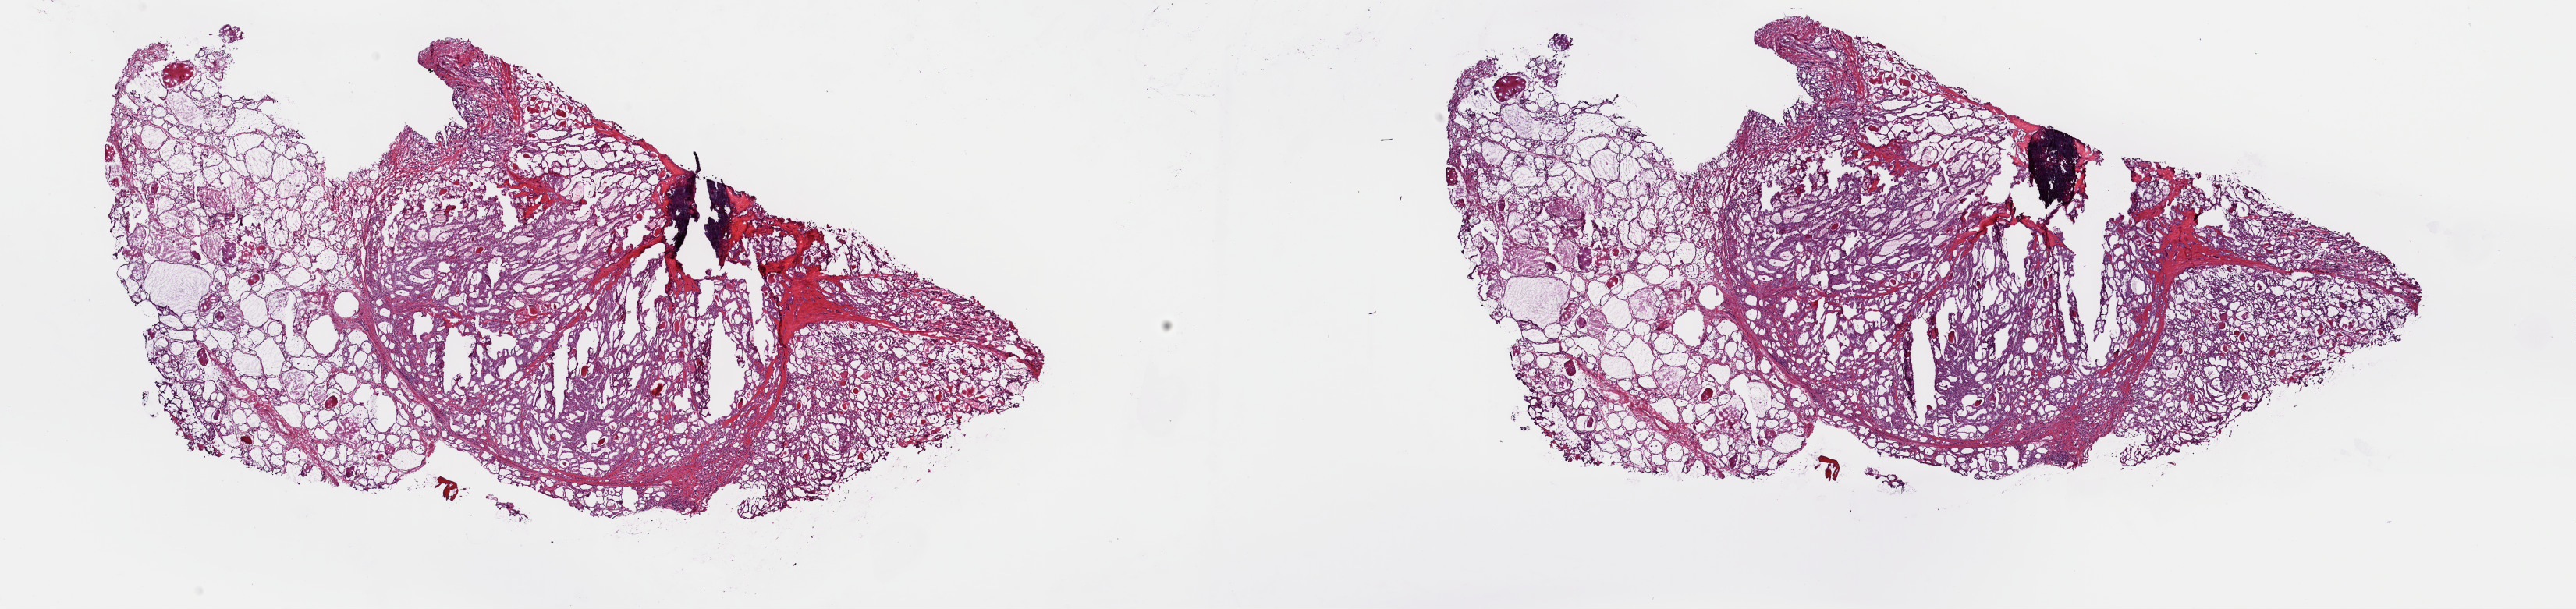
Digitized H&E tissue section (whole slide) — low-resolution overview of the scanned area, about 26.1 x 6.2 mm (acquisition: 40x scan), frozen section from the top of the tissue portion, thyroid, primary tumour sample. Female patient; age at initial diagnosis 70 years. Slide review estimates, as recorded: tumour cells 70%, tumour nuclei 75%, normal cells 30%, stromal cells 0%, necrosis 0%. Inflammatory infiltration, as recorded: lymphocyte infiltration 0%, monocyte infiltration 0%, neutrophil infiltration 0%.
TNM: T3 N0 M0. AJCC pathologic stage: III (7th edition). Laterality: bilateral. Diagnosis: Papillary adenocarcinoma, NOS (thyroid gland). Lymph nodes positive (case pathology): 0 of 3 examined.